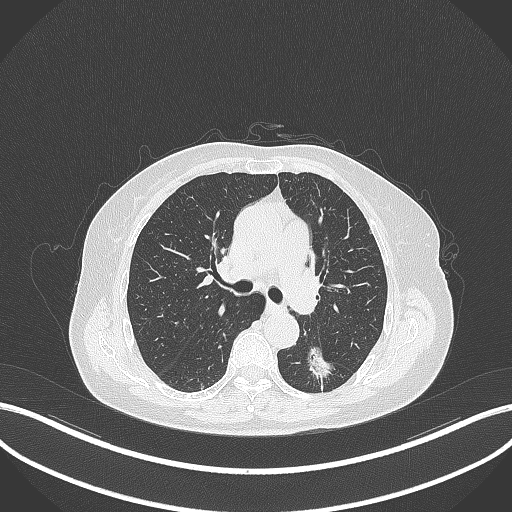
Chest CT, one axial slice. Position 184 of 352 along the scan axis. Lung window (W 1500 / L -600 HU). 1 mm slice thickness. 512 × 512 image matrix. Patient: female, 70 years. From the clinical record (not read from this slice): clinical TNM (as recorded): T1c N0 M0.
Annotated regions visible in this slice (rectangle marked by the reading radiologist):
- lung tumour (recorded histology: adenocarcinoma): bounding box <299,337,339,383> (left, top, right, bottom; pixels)